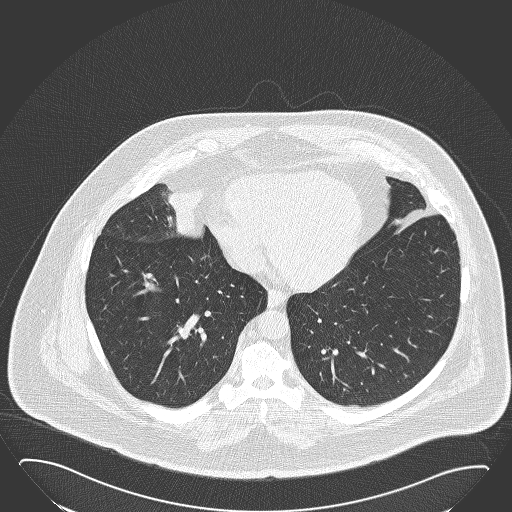
Chest CT (low-dose screening protocol), one axial image, baseline screening round, lung window (W 1500 / L -600 HU), 2 mm slice thickness, lung (sharp) reconstruction kernel (B50f), slice 109 of 168 in the series, 512 × 512 image matrix, field of view 432 × 432 mm. Male, age 61 years at enrolment. Former smoker at enrolment.
• Expert reader's lesion annotation, box from (x=127, y=160) to (x=226, y=252) px.
• The screening reader recorded 2 non-calcified nodules or masses ≥4 mm on this exam (right middle lobe, left lower lobe); which of them this box marks is not recorded.
• Official screen result: positive, change unspecified: nodule(s) >= 4 mm or enlarging nodule(s), mass(es), or other non-specific abnormalities suspicious for lung cancer.
• Later outcome: lung cancer diagnosed 47 days after this screen — basaloid squamous cell carcinoma, right middle lobe, right hilum, poorly differentiated (G3), stage IIB (AJCC 6th edition), 95 mm at pathology.